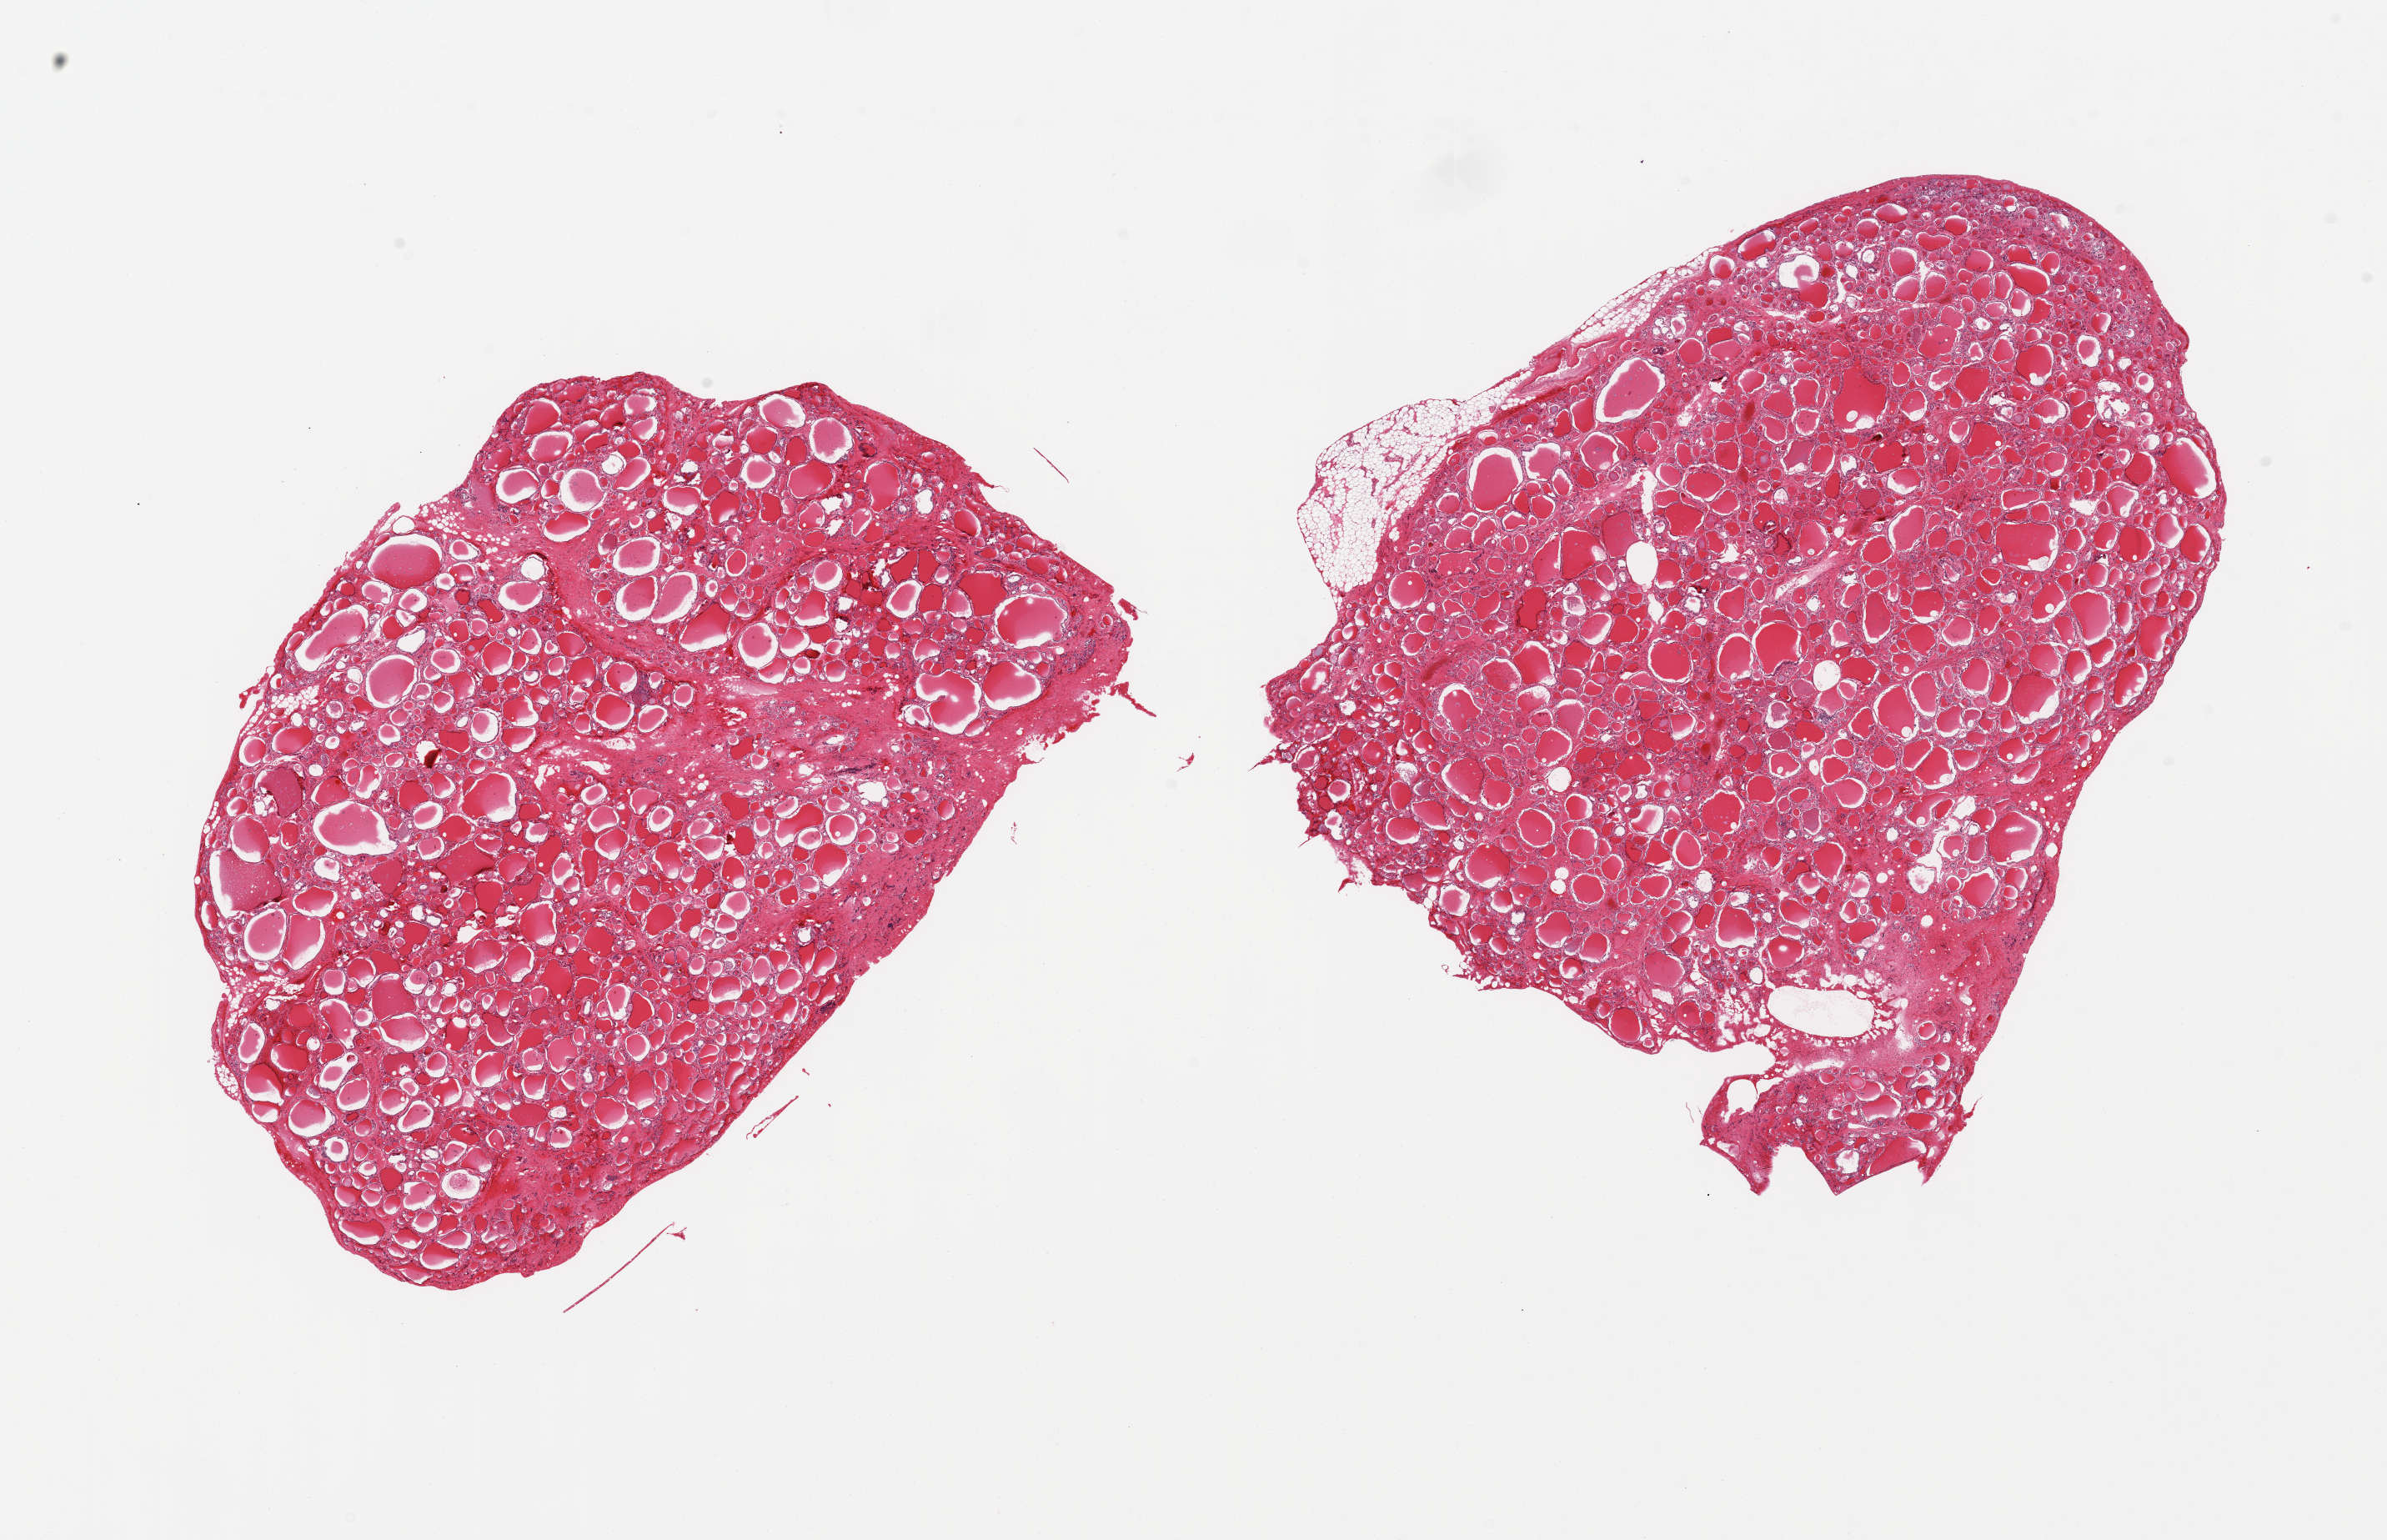
Digitized H&E-stained section, low-resolution overview of the scanned area, about 22.6 x 14.6 mm (slide scanned at 20x), PAXgene-fixed, paraffin-embedded tissue, section of thyroid (target tissue), donor tissue sample. Donor sex: male.
- reviewer comment on this tissue sample: 2 pieces, no abnormalities